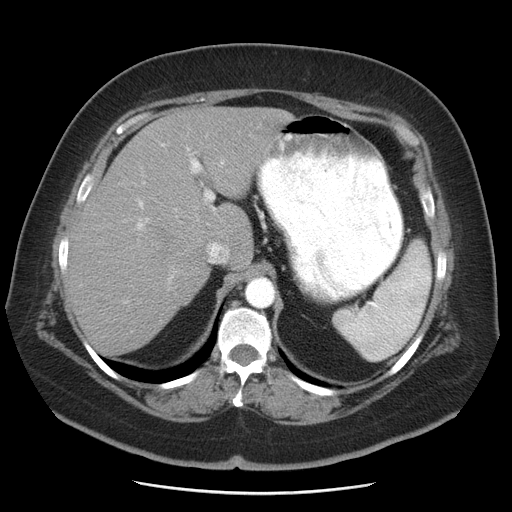
Contrast-enhanced abdominal CT, one axial slice. Reconstruction kernel STANDARD. 120 kVp. Soft-tissue window (W 400 / L 40 HU). 5 mm slice thickness. 512 × 512 image matrix, field of view 380 × 380 mm. Female patient, age 52 years. Case-level facts recorded for this patient, not image findings: diagnosis: colorectal cancer liver metastases, imaged before liver resection; multiple liver metastases: yes; largest metastasis: 2.5 cm; chemotherapy before resection: no.
Annotated regions visible in this slice (manually delineated by an expert):
- liver: bounding box (x1, y1, x2, y2) in pixels: (67, 107, 294, 356)
- planned liver remnant (the part of the liver to remain after resection): (67, 173, 209, 356)
- portal vein (with intrahepatic branches): (135, 143, 228, 281)